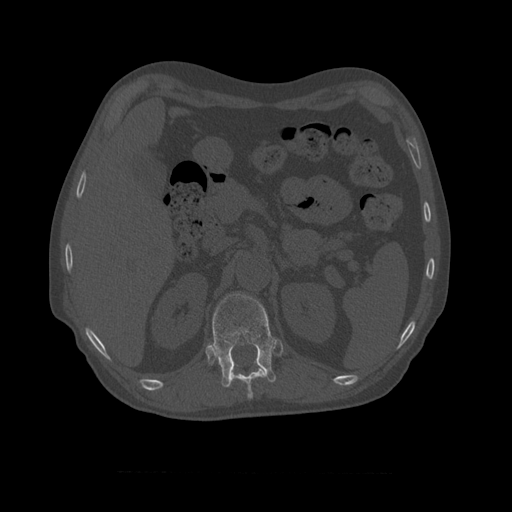
CT including the spine, one axial slice. Slice 384 of 450 in the series (ordered by position). Reconstruction kernel STANDARD. 120 kVp. Bone window (W 1800 / L 400 HU). 1.25 mm slice thickness. 512 × 512 image matrix, field of view 405 × 405 mm. Patient age 75 years. From the clinical record (not read from this slice): primary cancer: prostate.
Outlined on this slice (semi-automatic segmentation, software-assisted and operator-edited):
- T10 vertebra: bounding box [x1, y1, x2, y2] px = [230, 368, 266, 400]
- T11 vertebra: [209, 294, 277, 388]